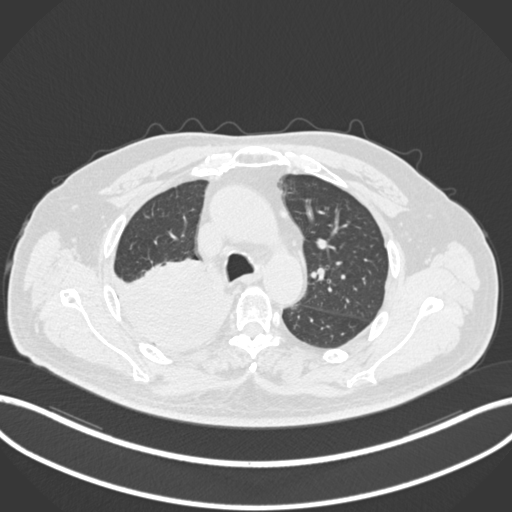
Chest CT, one axial slice. Position 145 of 218 along the scan axis. Reconstruction kernel B30f. 120 kVp. Lung window (W 1500 / L -600 HU). 512 × 512 image matrix, field of view 400 × 400 mm. Male patient, age 68 years. From the clinical record (not read from this slice): clinical TNM (as recorded): T2a N0 M0.
Annotated regions visible in this slice (rectangle marked by the reading radiologist):
- lung tumour (recorded histology: adenocarcinoma): bounding box <116,257,237,356> (left, top, right, bottom; pixels)